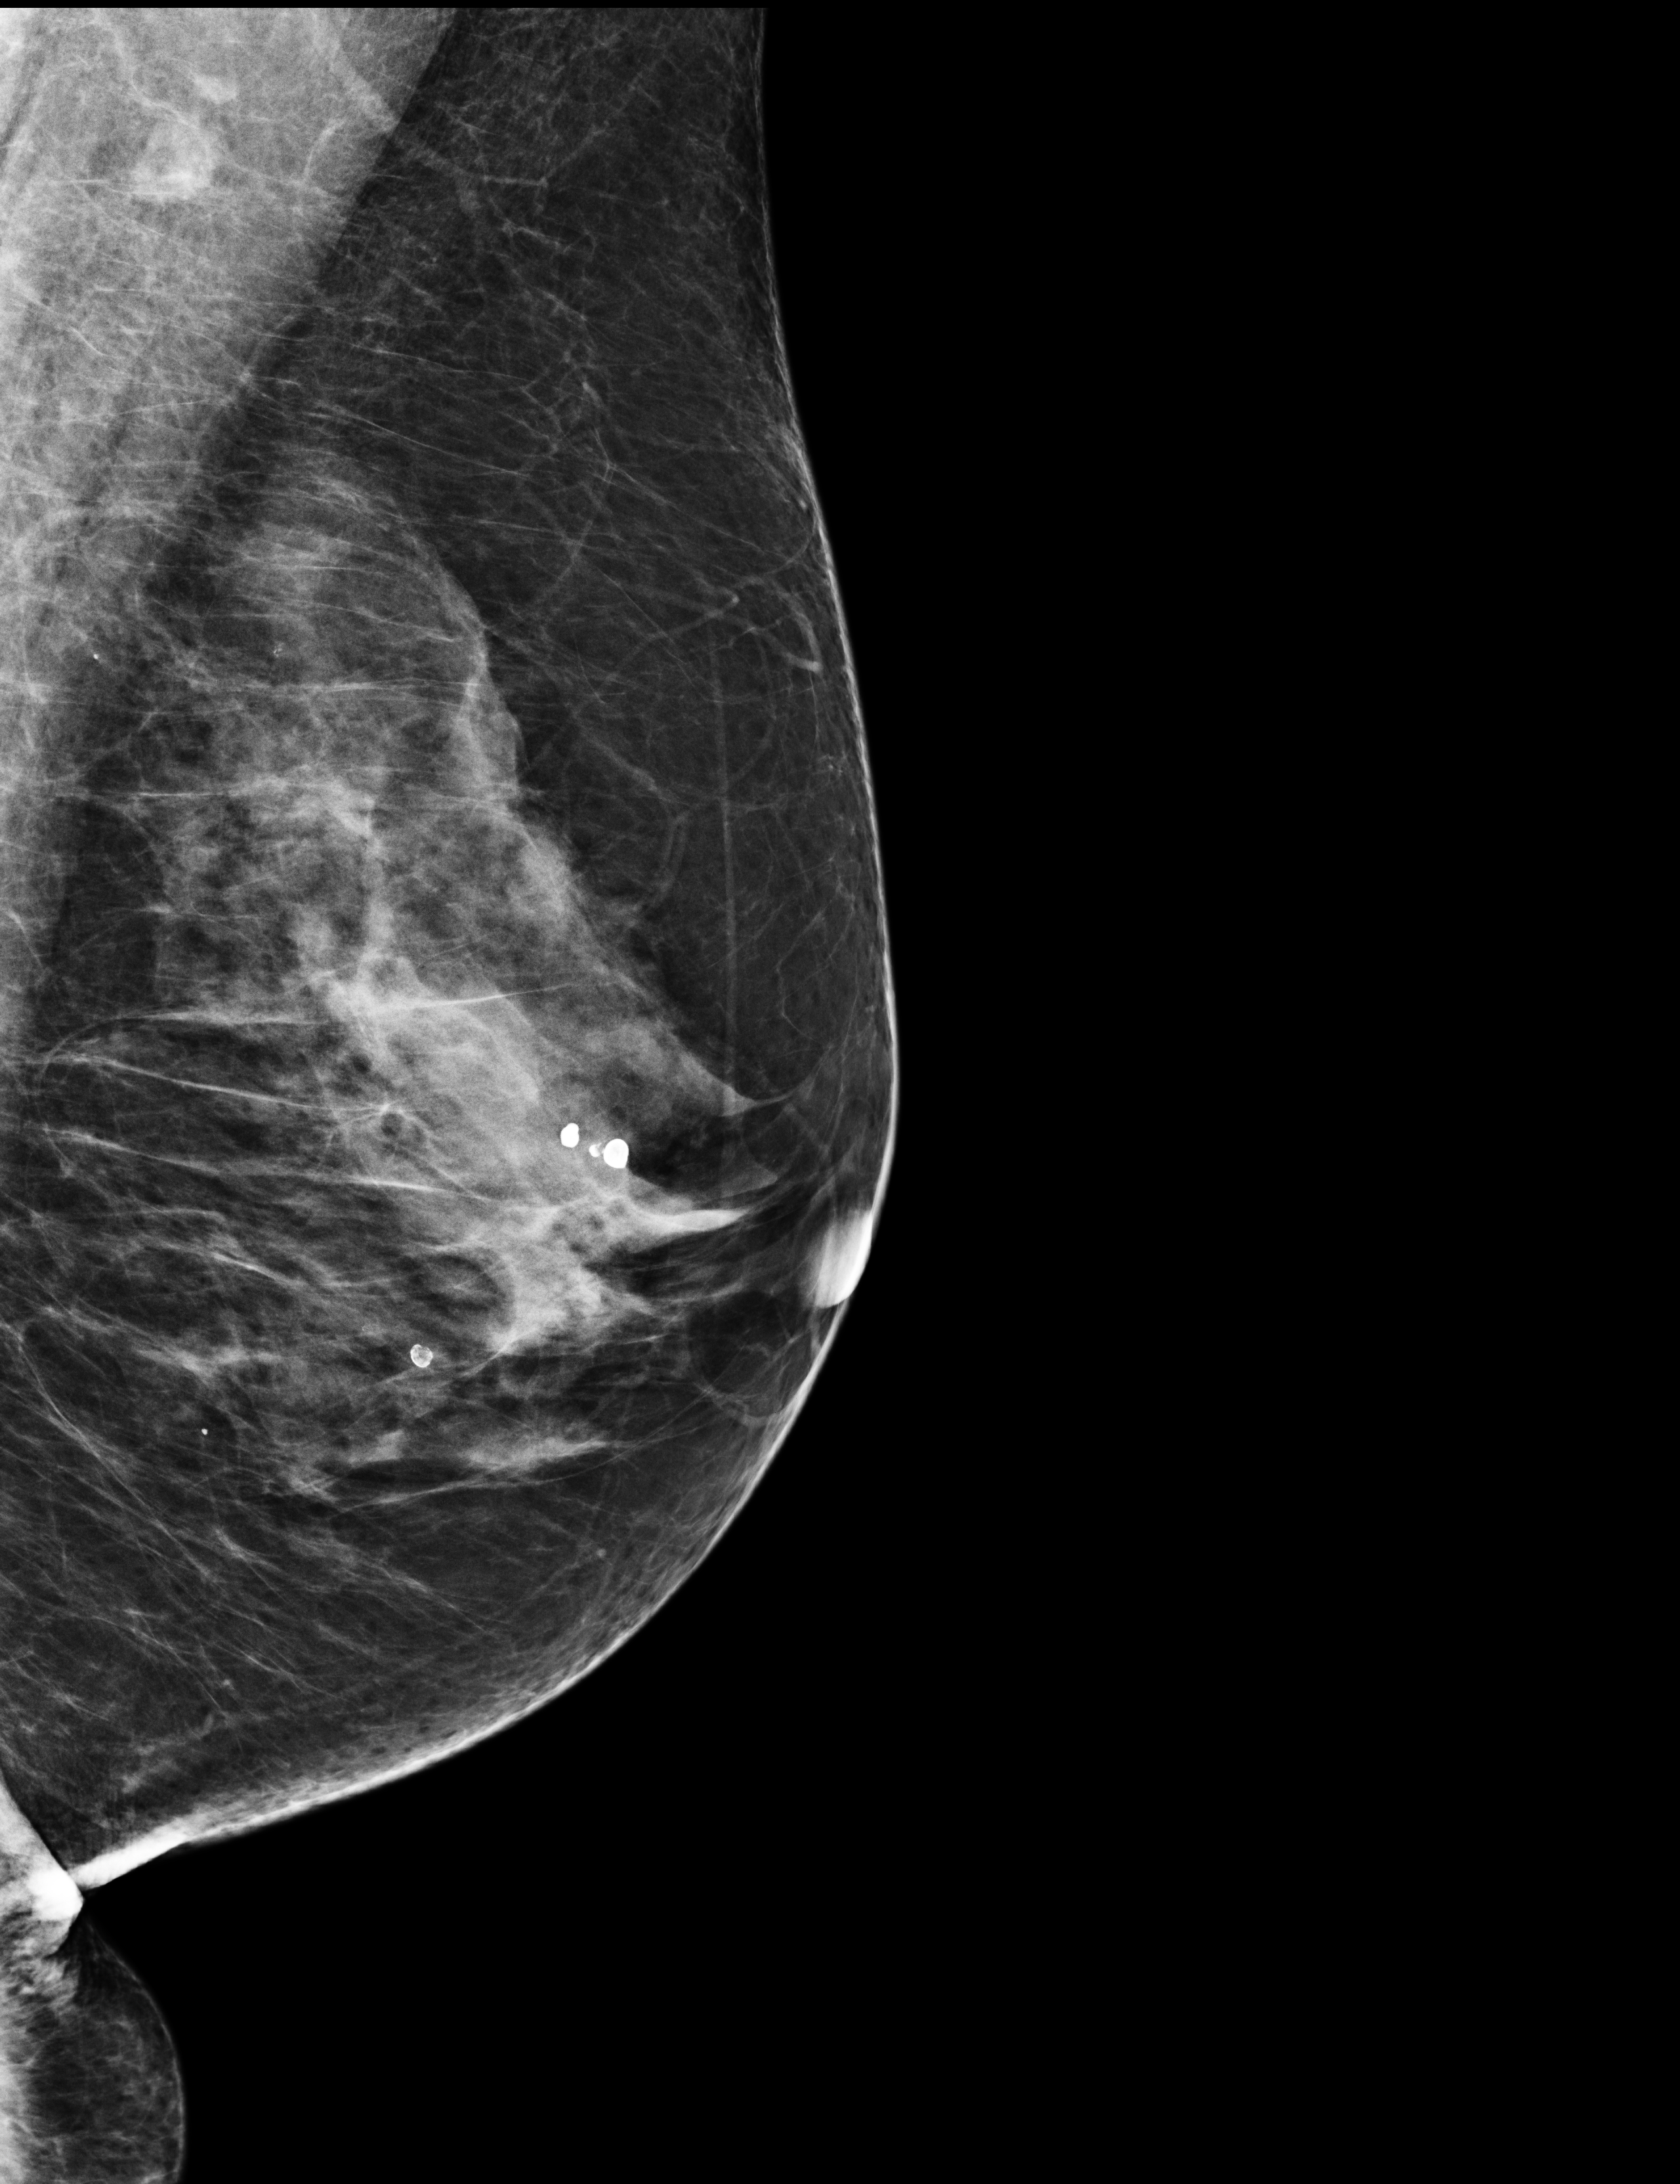
Screening examination; compressed breast thickness 59 mm; system: Selenia Dimensions. Female patient, age 67 years.
Image type: full-field digital mammogram. Breast: left. Projection: MLO view.